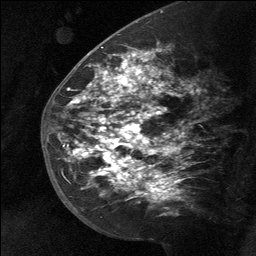
Breast MRI (dynamic contrast-enhanced), one sagittal slice. Position 38 of 64 along the scan axis. Dynamic contrast-enhanced study with each time point stored as its own series, time point 2 of 3 at this slice position (early post-contrast, ordered by acquisition time). 1.5 T. TE 4.8 ms, TR 27 ms. 2 mm slice thickness. 256 × 256 image matrix, field of view 180 × 180 mm. Female patient, age 39 years. Case-level facts recorded for this patient, not image findings: setting: breast cancer imaged before/during neoadjuvant chemotherapy; receptor status: HER2-positive.
Outlined on this slice (semi-automatically segmented with operator editing):
- analysis volume of interest (the breast-tissue region the enhancement analysis was run in; not a lesion): bounding box [x1, y1, x2, y2] px = [58, 40, 185, 217]
- tumour enhancement mask (voxels above the 90 % enhancement threshold inside the analysis volume of interest): [71, 52, 166, 196]